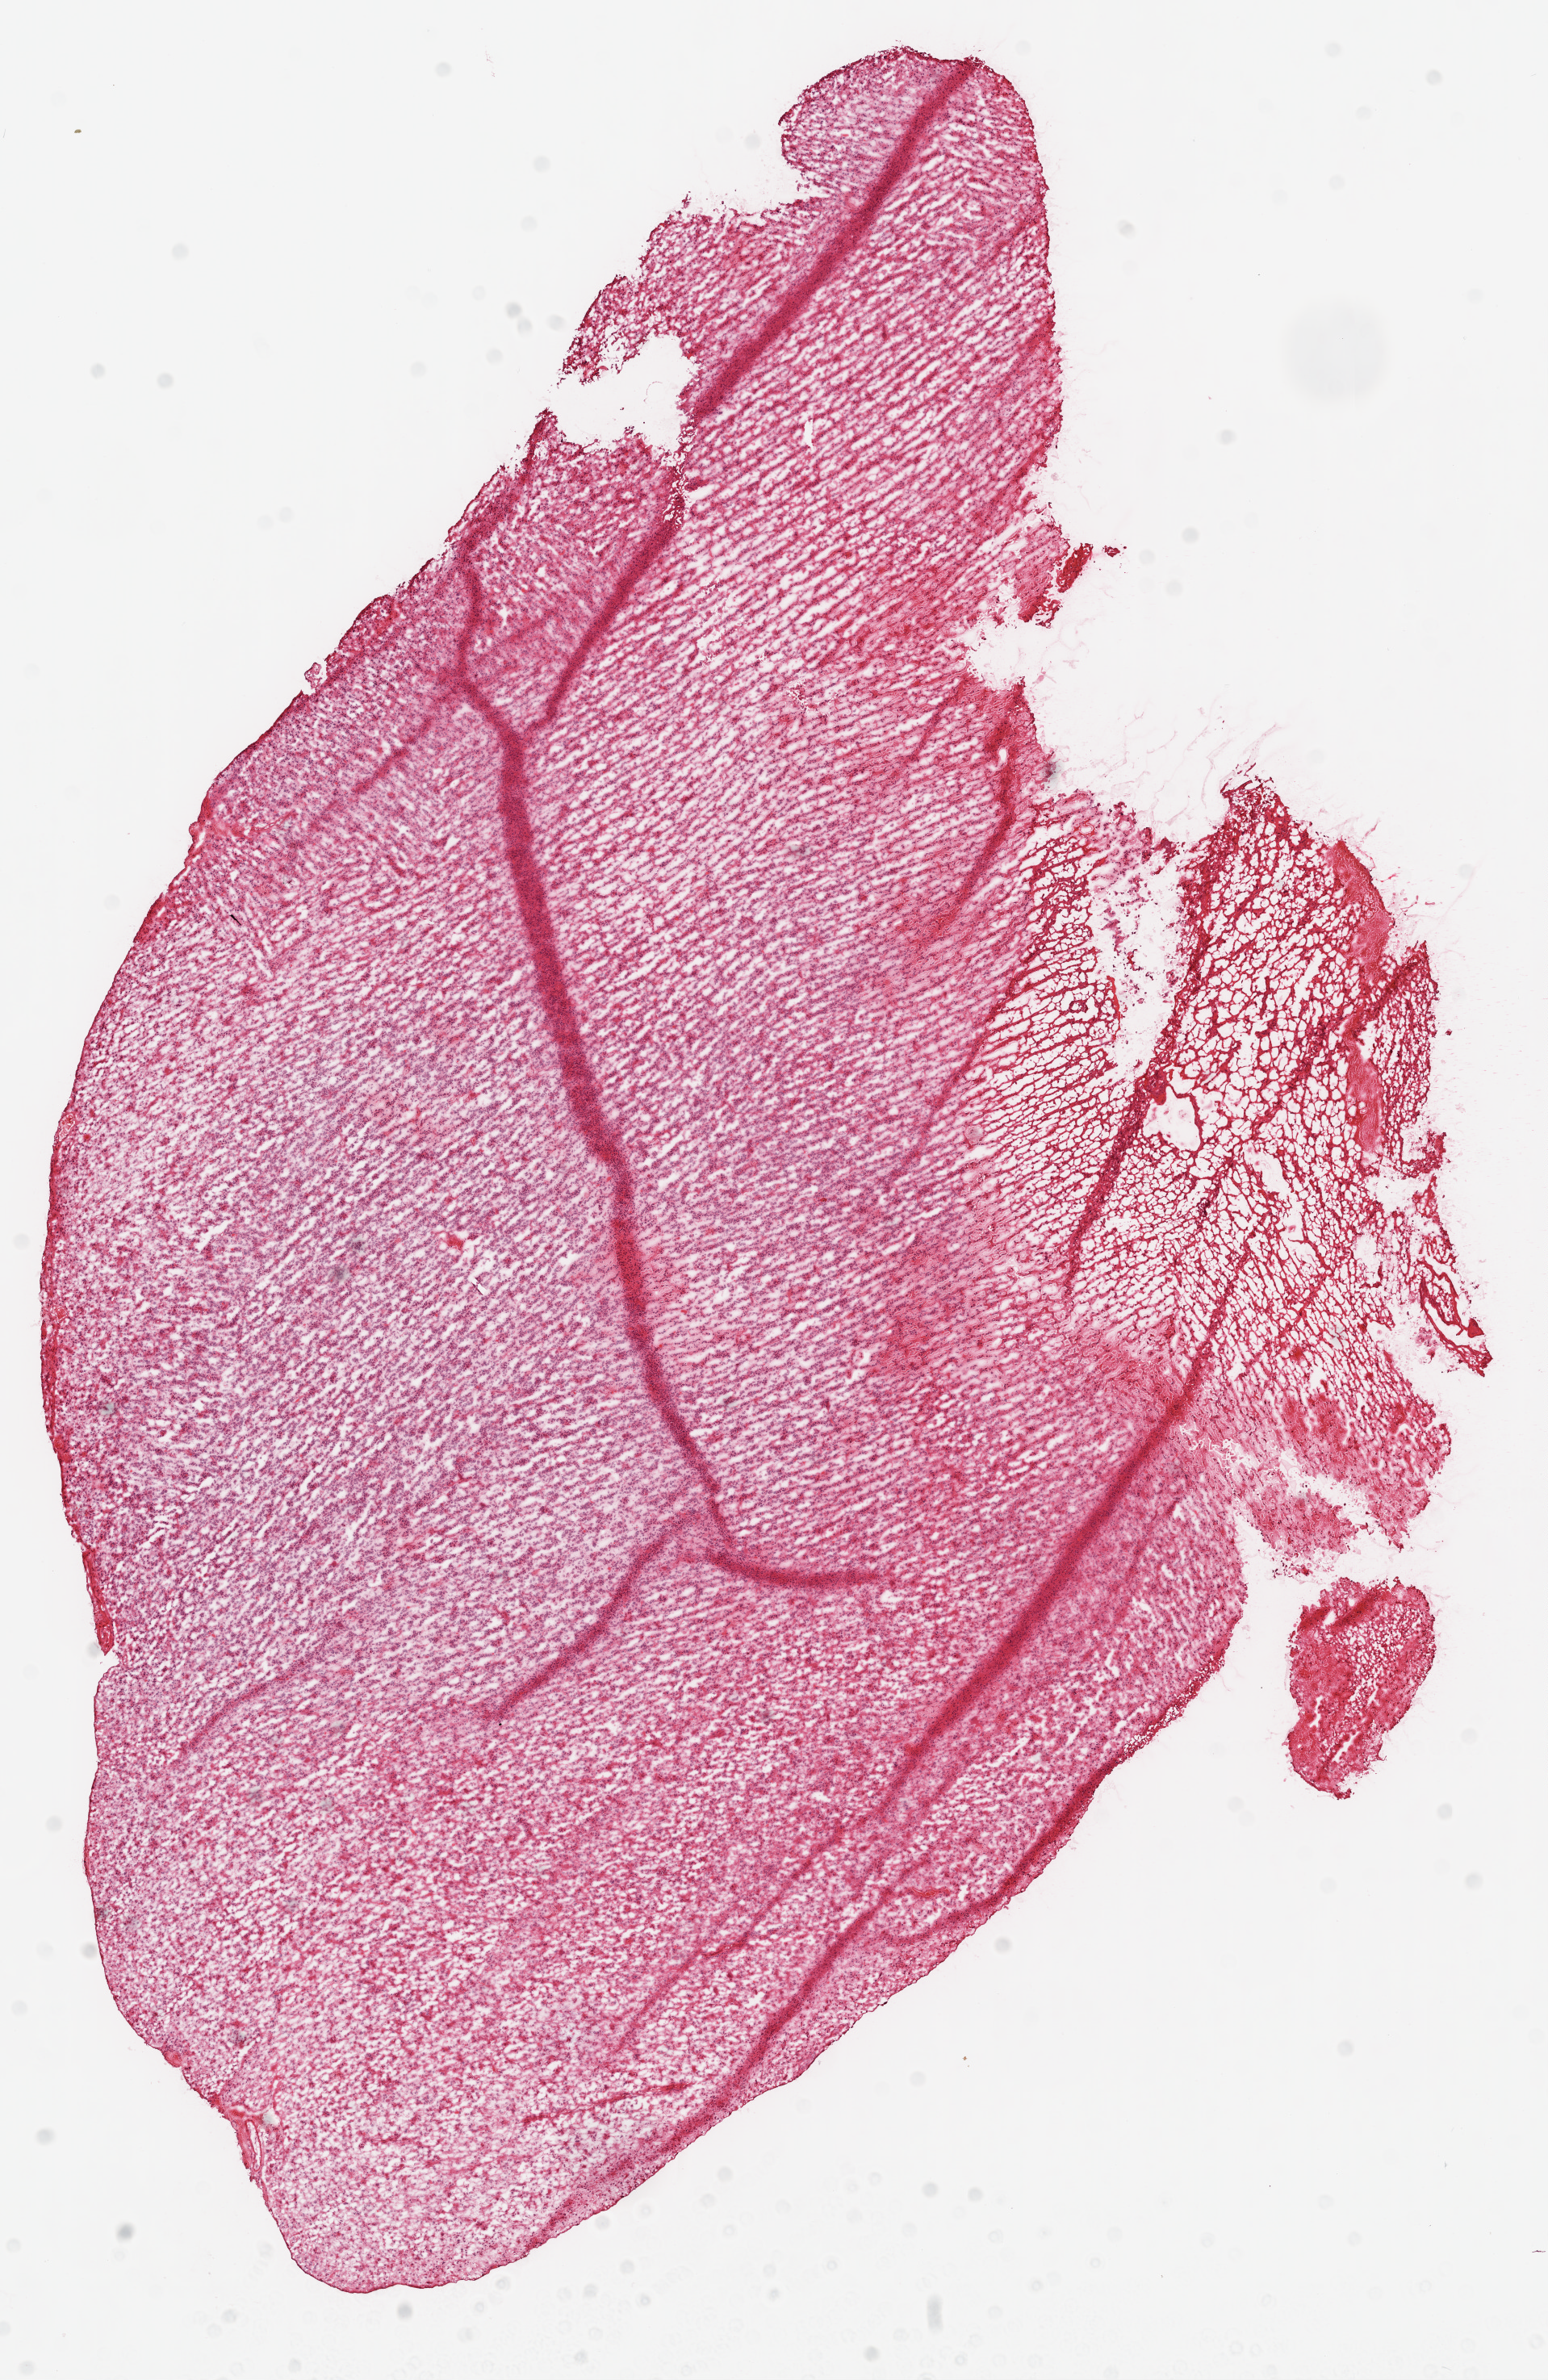
Digitized H&E-stained tissue section (whole slide), a low-resolution overview of the entire scanned area, about 7.7 x 11.9 mm (slide scanned at 20x), frozen section from the top of the tissue portion, primary tumour sample from the brain. Female, age 36 years at initial diagnosis.
Pathologic diagnosis: Glioblastoma.